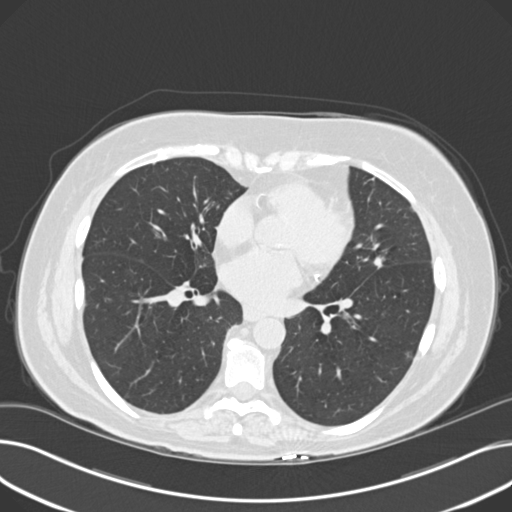
Low-dose screening chest CT, one axial slice; reconstruction kernel B30f; lung window (W 1500 / L -600 HU); 2 mm slice thickness; 512 × 512 image matrix.
Outlined on this slice (manually delineated by an expert):
- lesion 1 (tumor, upper lobe of left lung): box from (x=373, y=256) to (x=384, y=269) px